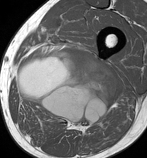
MRI of an extremity soft-tissue mass, one axial slice; slice 56 of 86 in the series (ordered by position); MR volume resampled by the dataset authors to the PET/CT grid (not the native acquisition matrix); 3.27 mm slice thickness; 147 × 158 image matrix, field of view 144 × 154 mm. Male patient. Case-level facts recorded for this patient, not image findings: histological type: undifferentiated pleomorphic liposarcoma; grade: high; site of the primary tumour: left thigh.
Annotated regions visible in this slice (expert contour drawn on MRI and transferred to this co-registered scan by the dataset authors):
- gross tumour volume including surrounding oedema: box from (x=16, y=49) to (x=118, y=130) px
- gross tumour volume (mass): (x=16, y=49)–(x=118, y=127)